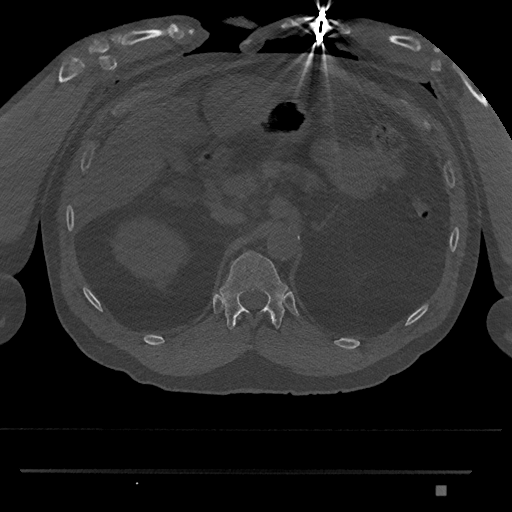
CT including the spine, one axial slice; slice 901 of 1134 in the series (ordered by position); bone window (W 1800 / L 400 HU); 0.5 mm slice thickness; 512 × 512 image matrix, field of view 429 × 429 mm. Patient: male, 65 years. From the clinical record (not read from this slice): primary cancer: prostate.
Outlined on this slice (semi-automatically segmented with operator editing):
- T11 vertebra: bounding box (x1, y1, x2, y2) in pixels: (248, 345, 253, 349)
- T12 vertebra: (219, 251, 288, 331)